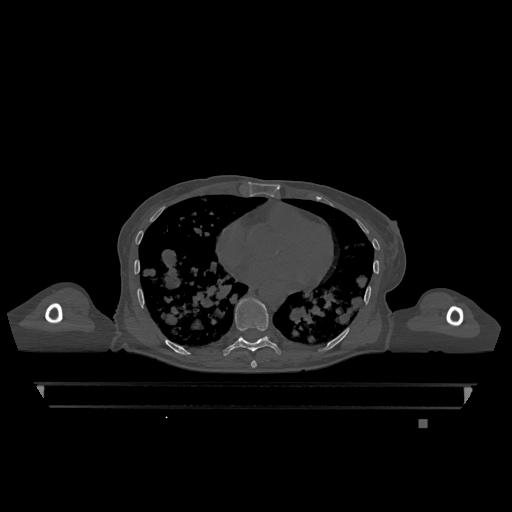
CT including the spine, one axial slice. Position 689 of 1317 along the scan axis. Bone window (W 1800 / L 400 HU). 512 × 512 image matrix, field of view 500 × 500 mm. Patient: female, 74 years. From the clinical record (not read from this slice): primary cancer: lung.
Structures marked on this image (semi-automatic segmentation, software-assisted and operator-edited):
- T7 vertebra: bounding box (x1, y1, x2, y2) in pixels: (251, 360, 257, 368)
- T9 vertebra: (223, 297, 281, 356)